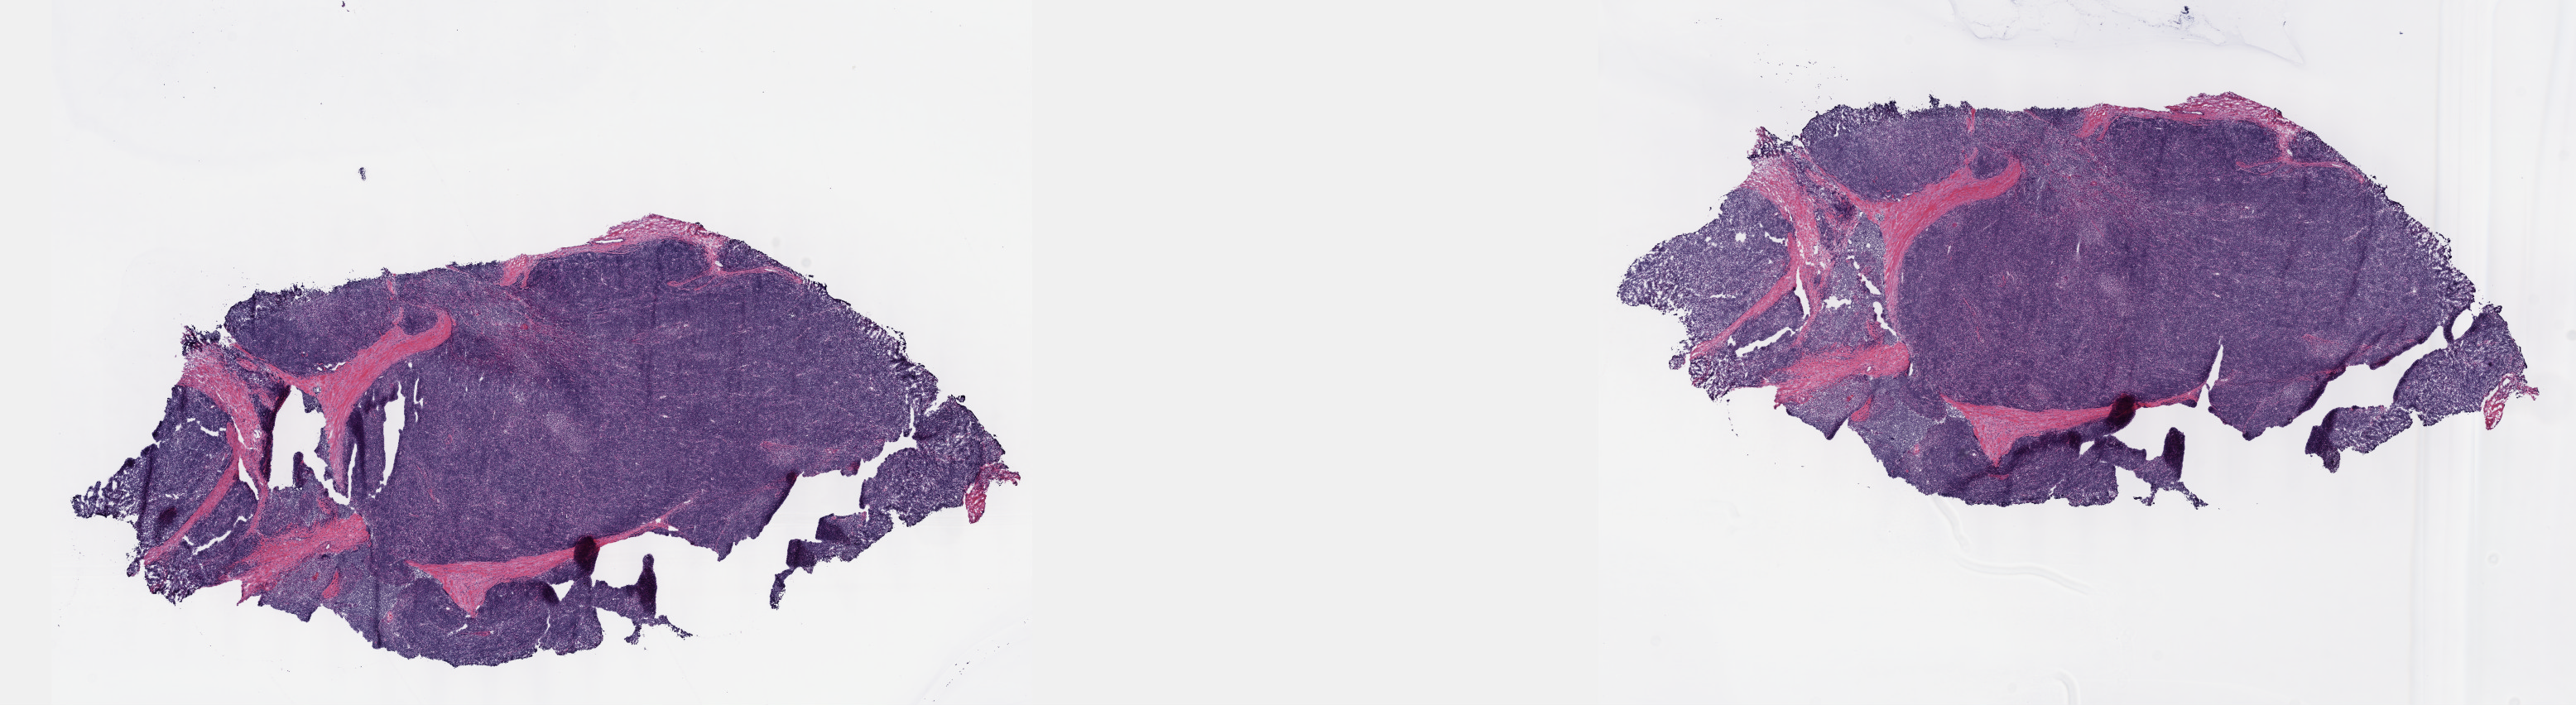
Whole-slide histology image, H&E-stained, whole scanned area (about 25.1 x 6.9 mm, slide scanned at 40x) shown as a low-resolution overview; frozen section; primary tumour sample from the thymus. Male, age 52 years at initial diagnosis. Composition of this section per pathologist review: tumour cells 90%, tumour nuclei 95%, normal cells 0%, stromal cells 10%, necrosis 0%. Inflammatory infiltration, as recorded: lymphocyte infiltration 0%, monocyte infiltration 0%, neutrophil infiltration 0%.
- histologic diagnosis: Thymoma, type B2, malignant (anterior mediastinum)